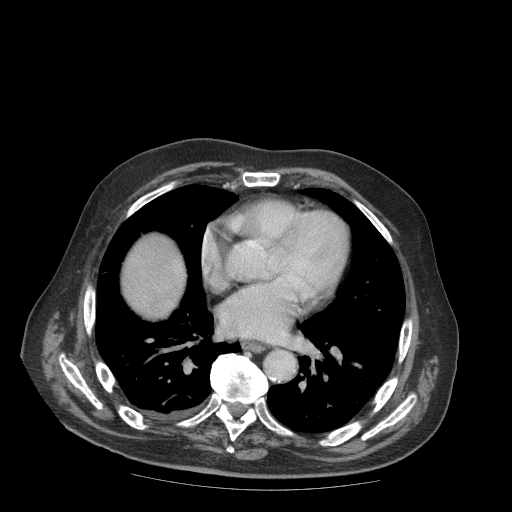
Contrast-enhanced abdominal CT (liver protocol), one axial slice; position 95 of 99 along the scan axis; reconstruction kernel STANDARD; 140 kVp; soft-tissue window (W 400 / L 40 HU); 512 × 512 image matrix, field of view 420 × 420 mm. From the clinical record (not read from this slice): diagnosis: hepatocellular carcinoma (patient treated with transarterial chemoembolisation; whether this scan precedes or follows treatment is not stated here); TNM stage (as recorded): Stage-IIIB; Child-Pugh class: A; tumour differentiation: well differentiated.
Annotated regions visible in this slice (semi-automatically segmented with operator editing):
- liver parenchyma outside the tumour (the mass and vessels are separate outlines, so this box may not span the whole liver): bounding box (x1, y1, x2, y2) in pixels: (122, 234, 186, 318)